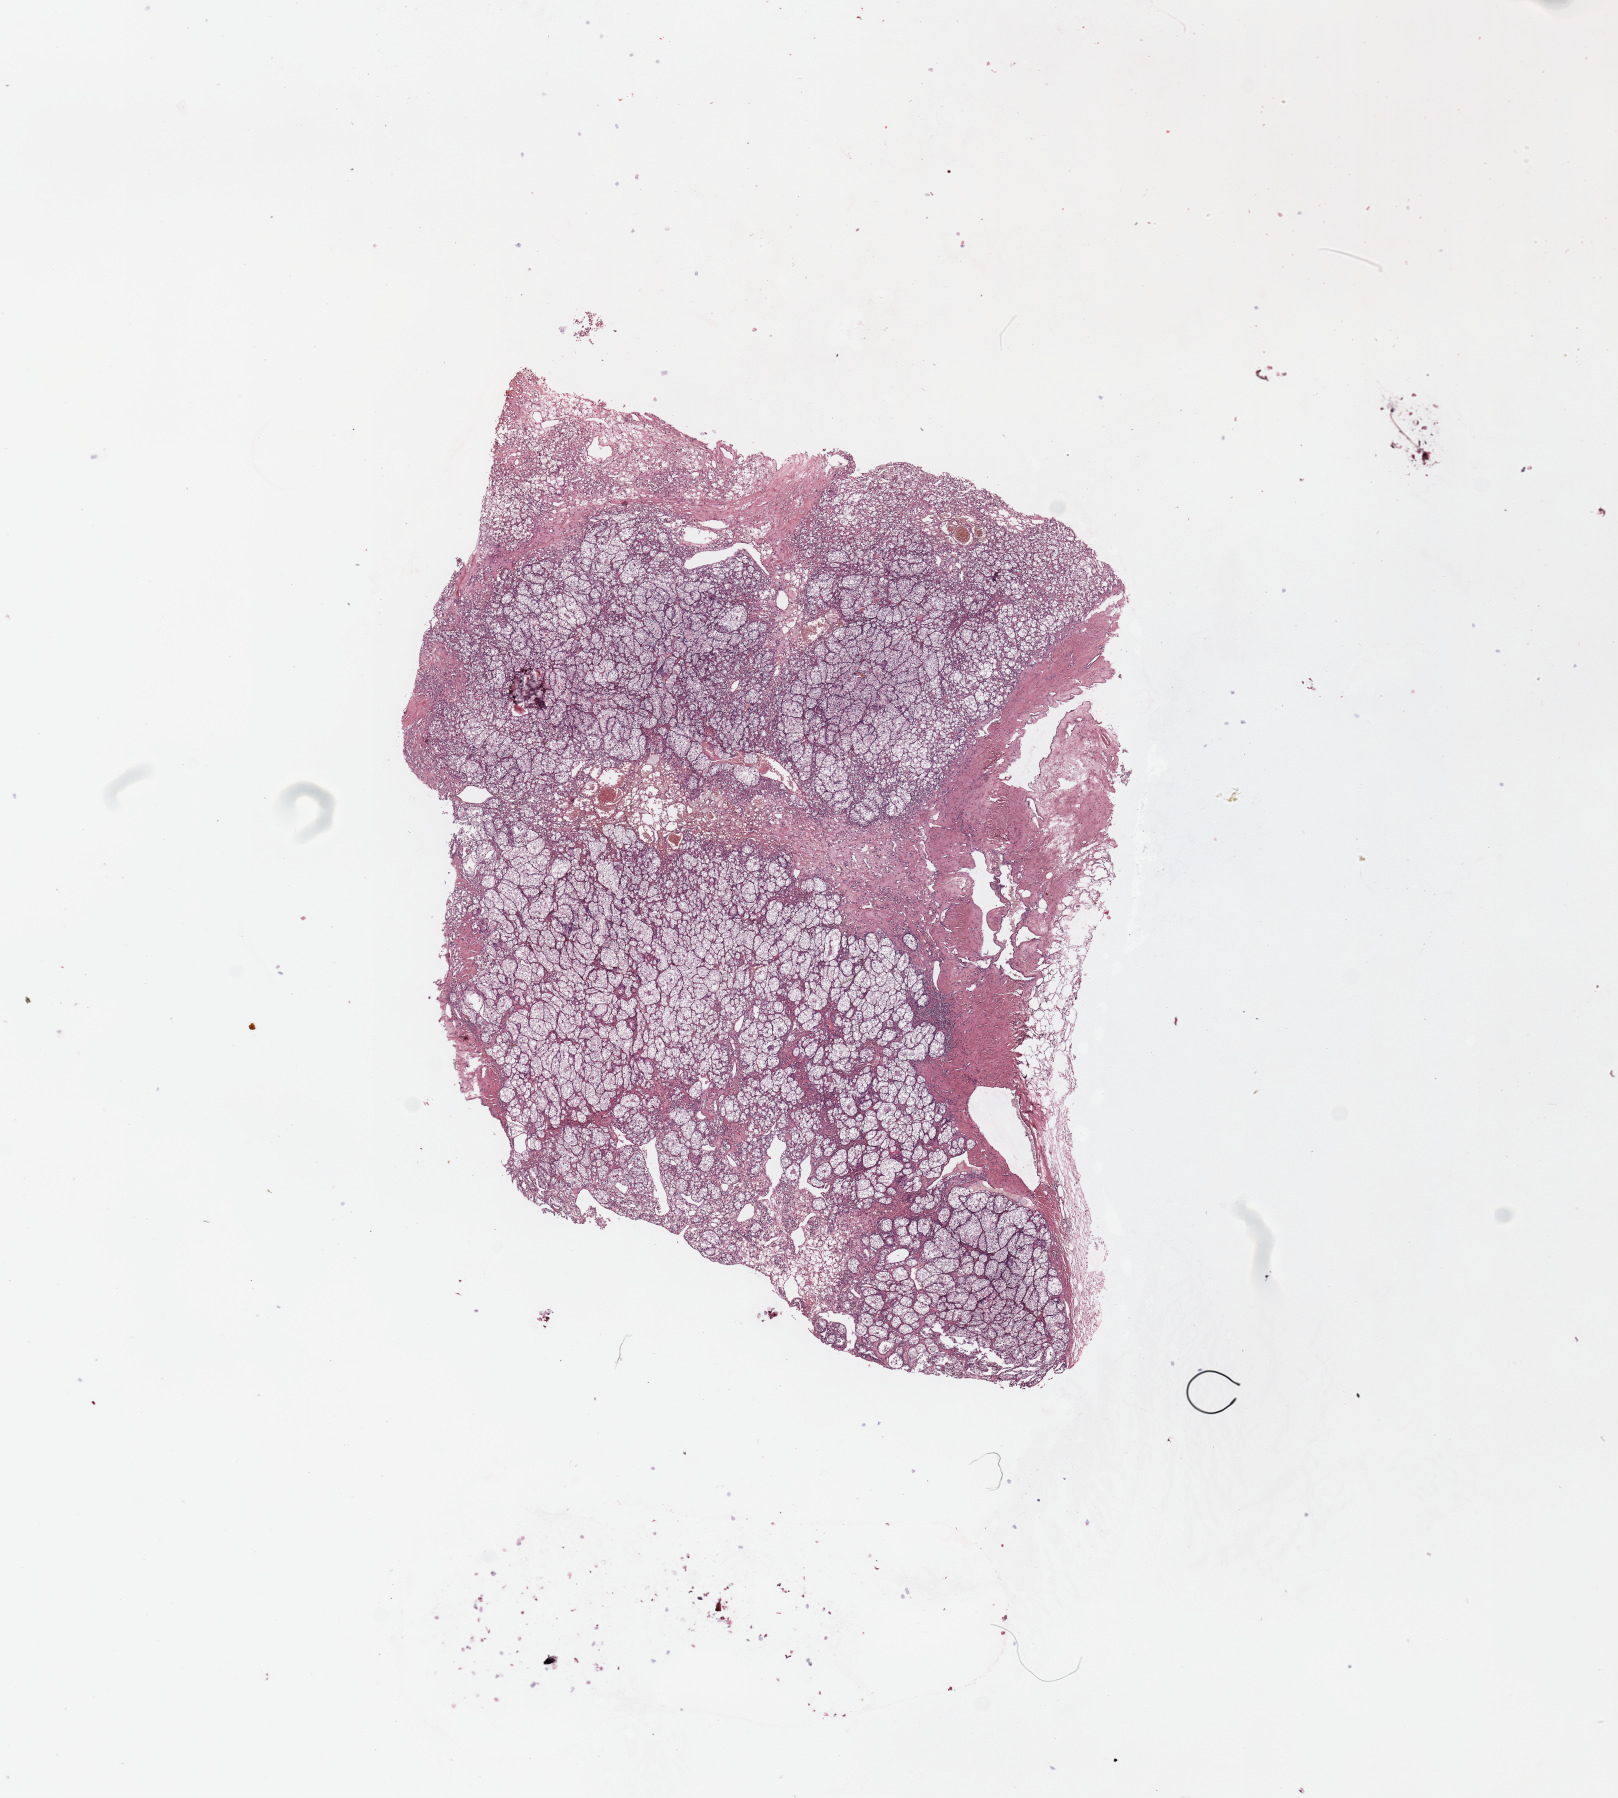
Digitized H&E tissue section (whole slide), whole scanned area (about 12.8 x 14.2 mm, acquisition: 20x scan) shown as a low-resolution overview; kidney, tumour tissue. Male, 68 y/o. Histologic grade: G1 (well differentiated).
AJCC pathologic stage: III. Histologic diagnosis: Renal cell carcinoma, NOS. Primary tumour site (as recorded): upper pole.